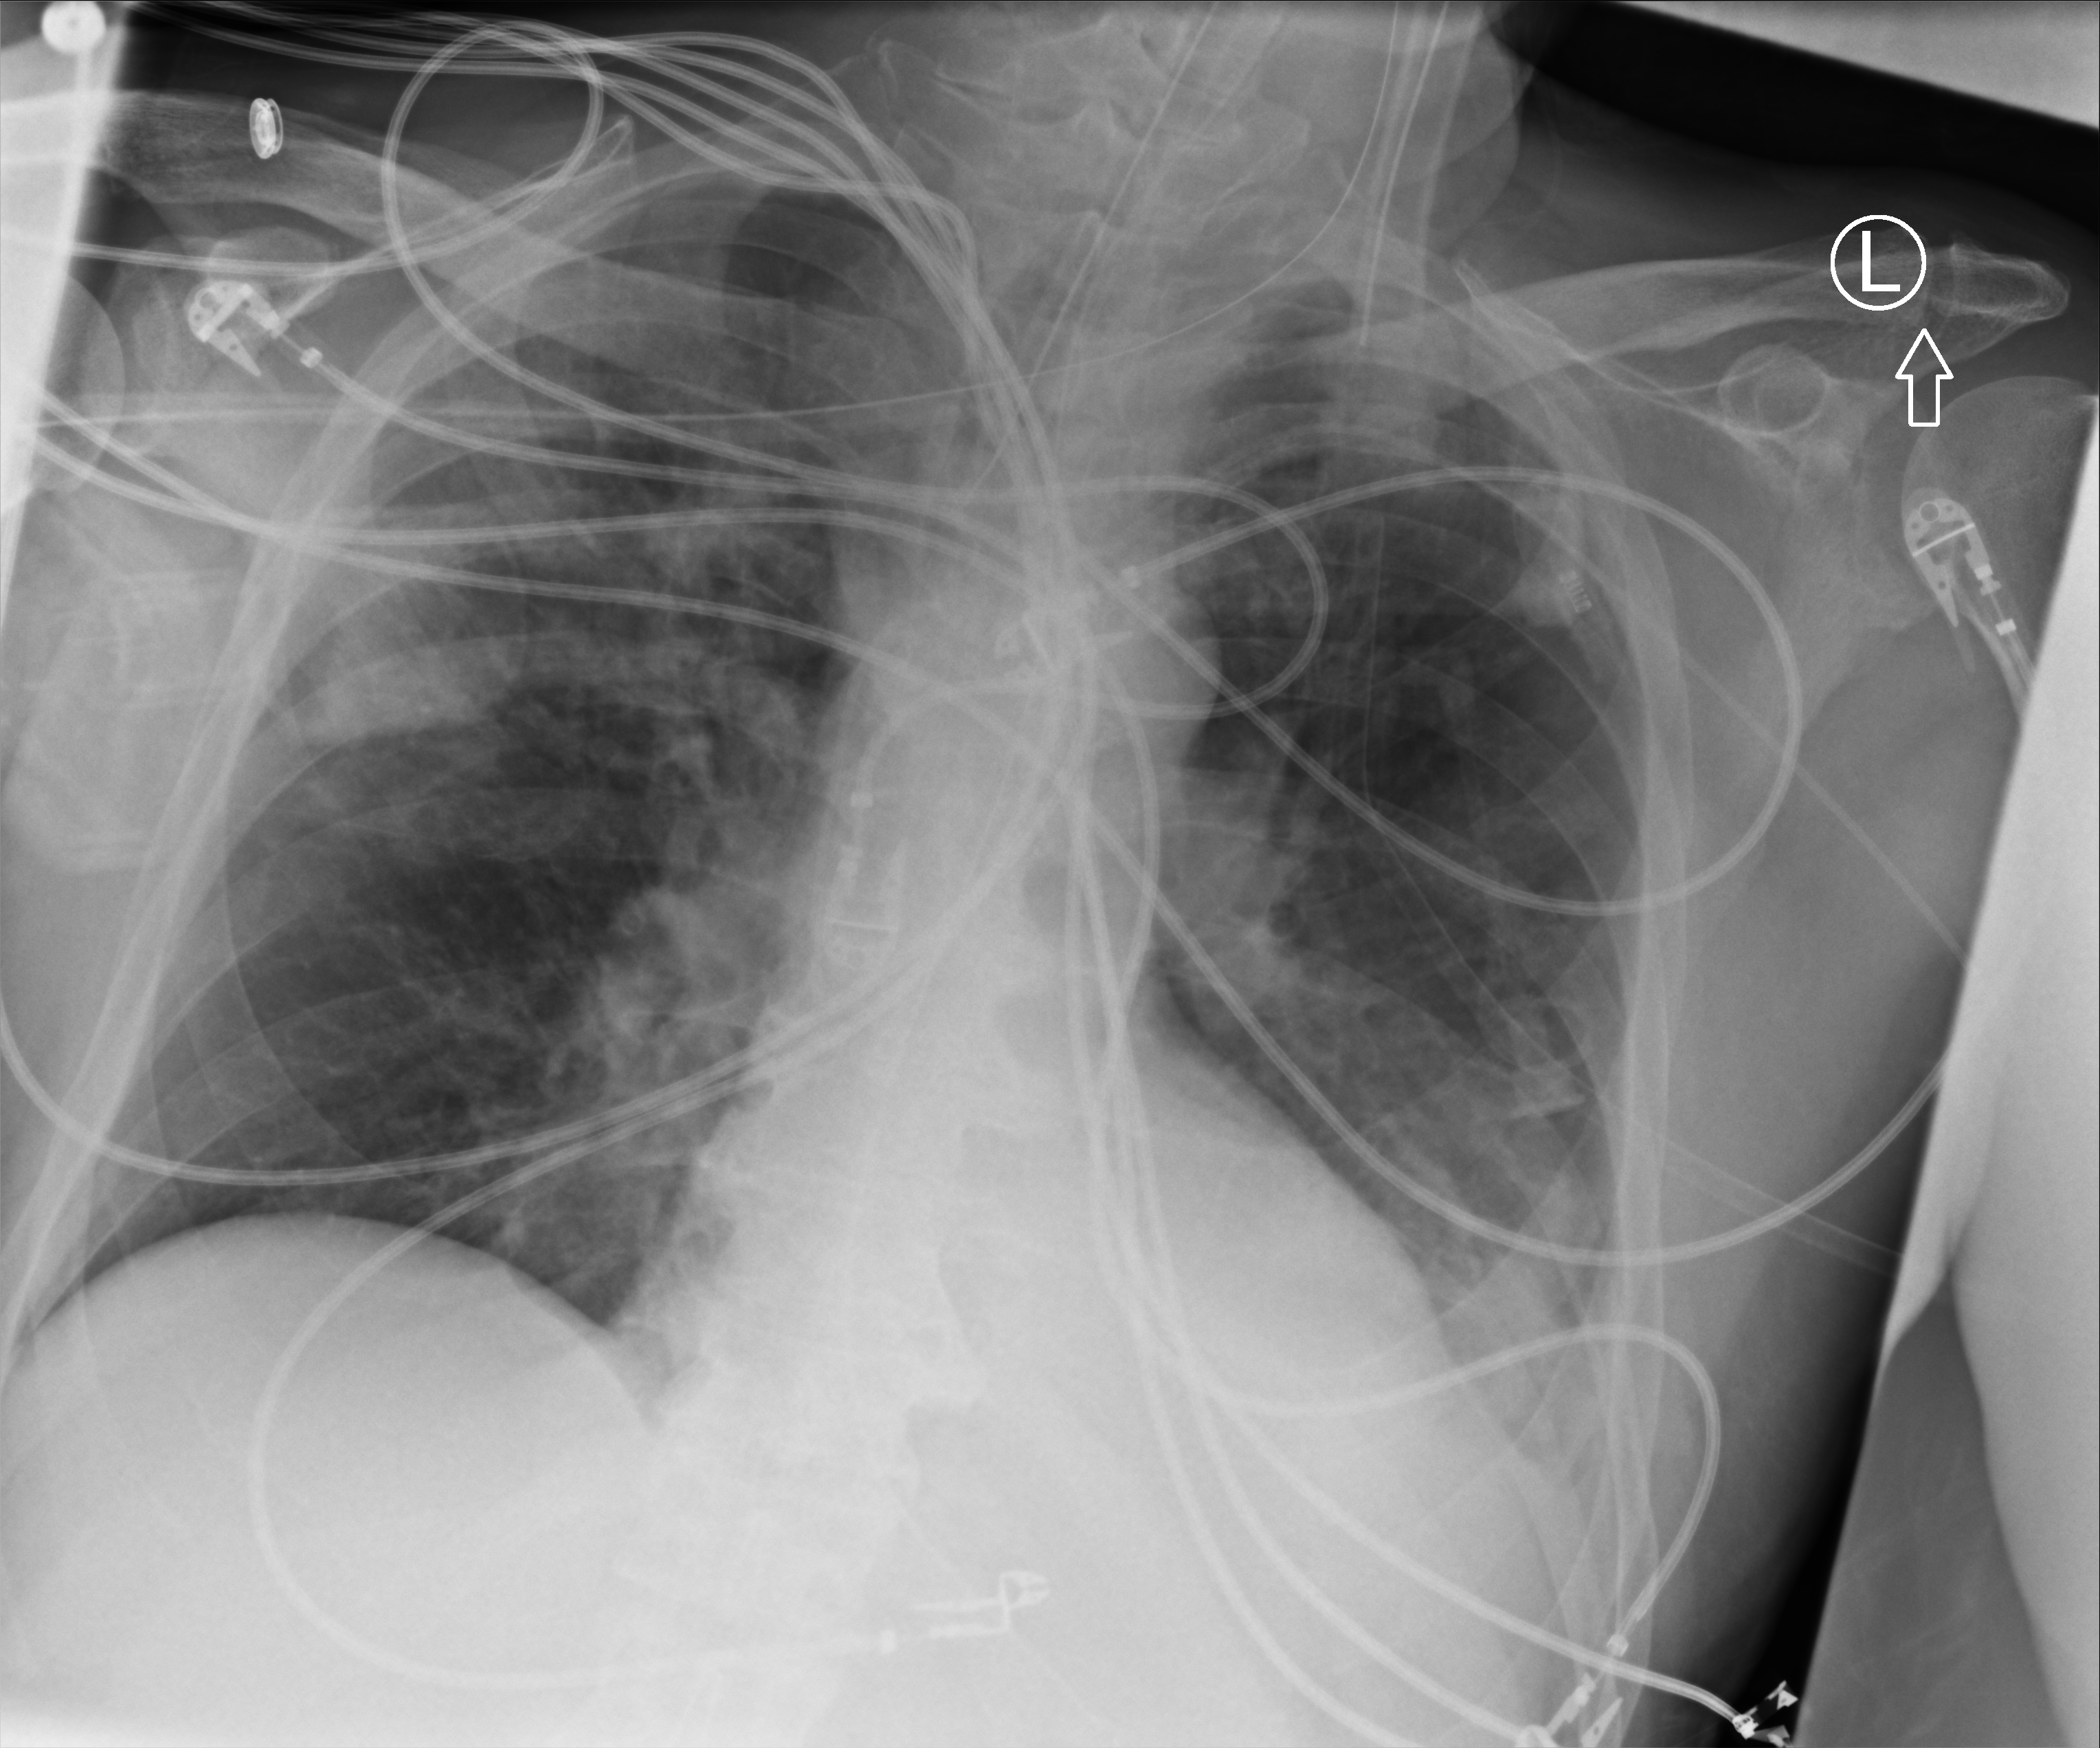
Chest X-ray (portable), anteroposterior (AP) projection. Male patient hospitalised with COVID-19, age 60–74 years.
From the hospital-stay record, not from the radiograph (when in the stay this image was taken is not recorded):
- mechanically ventilated during this hospital stay: yes
- chronic kidney disease (admission record): no